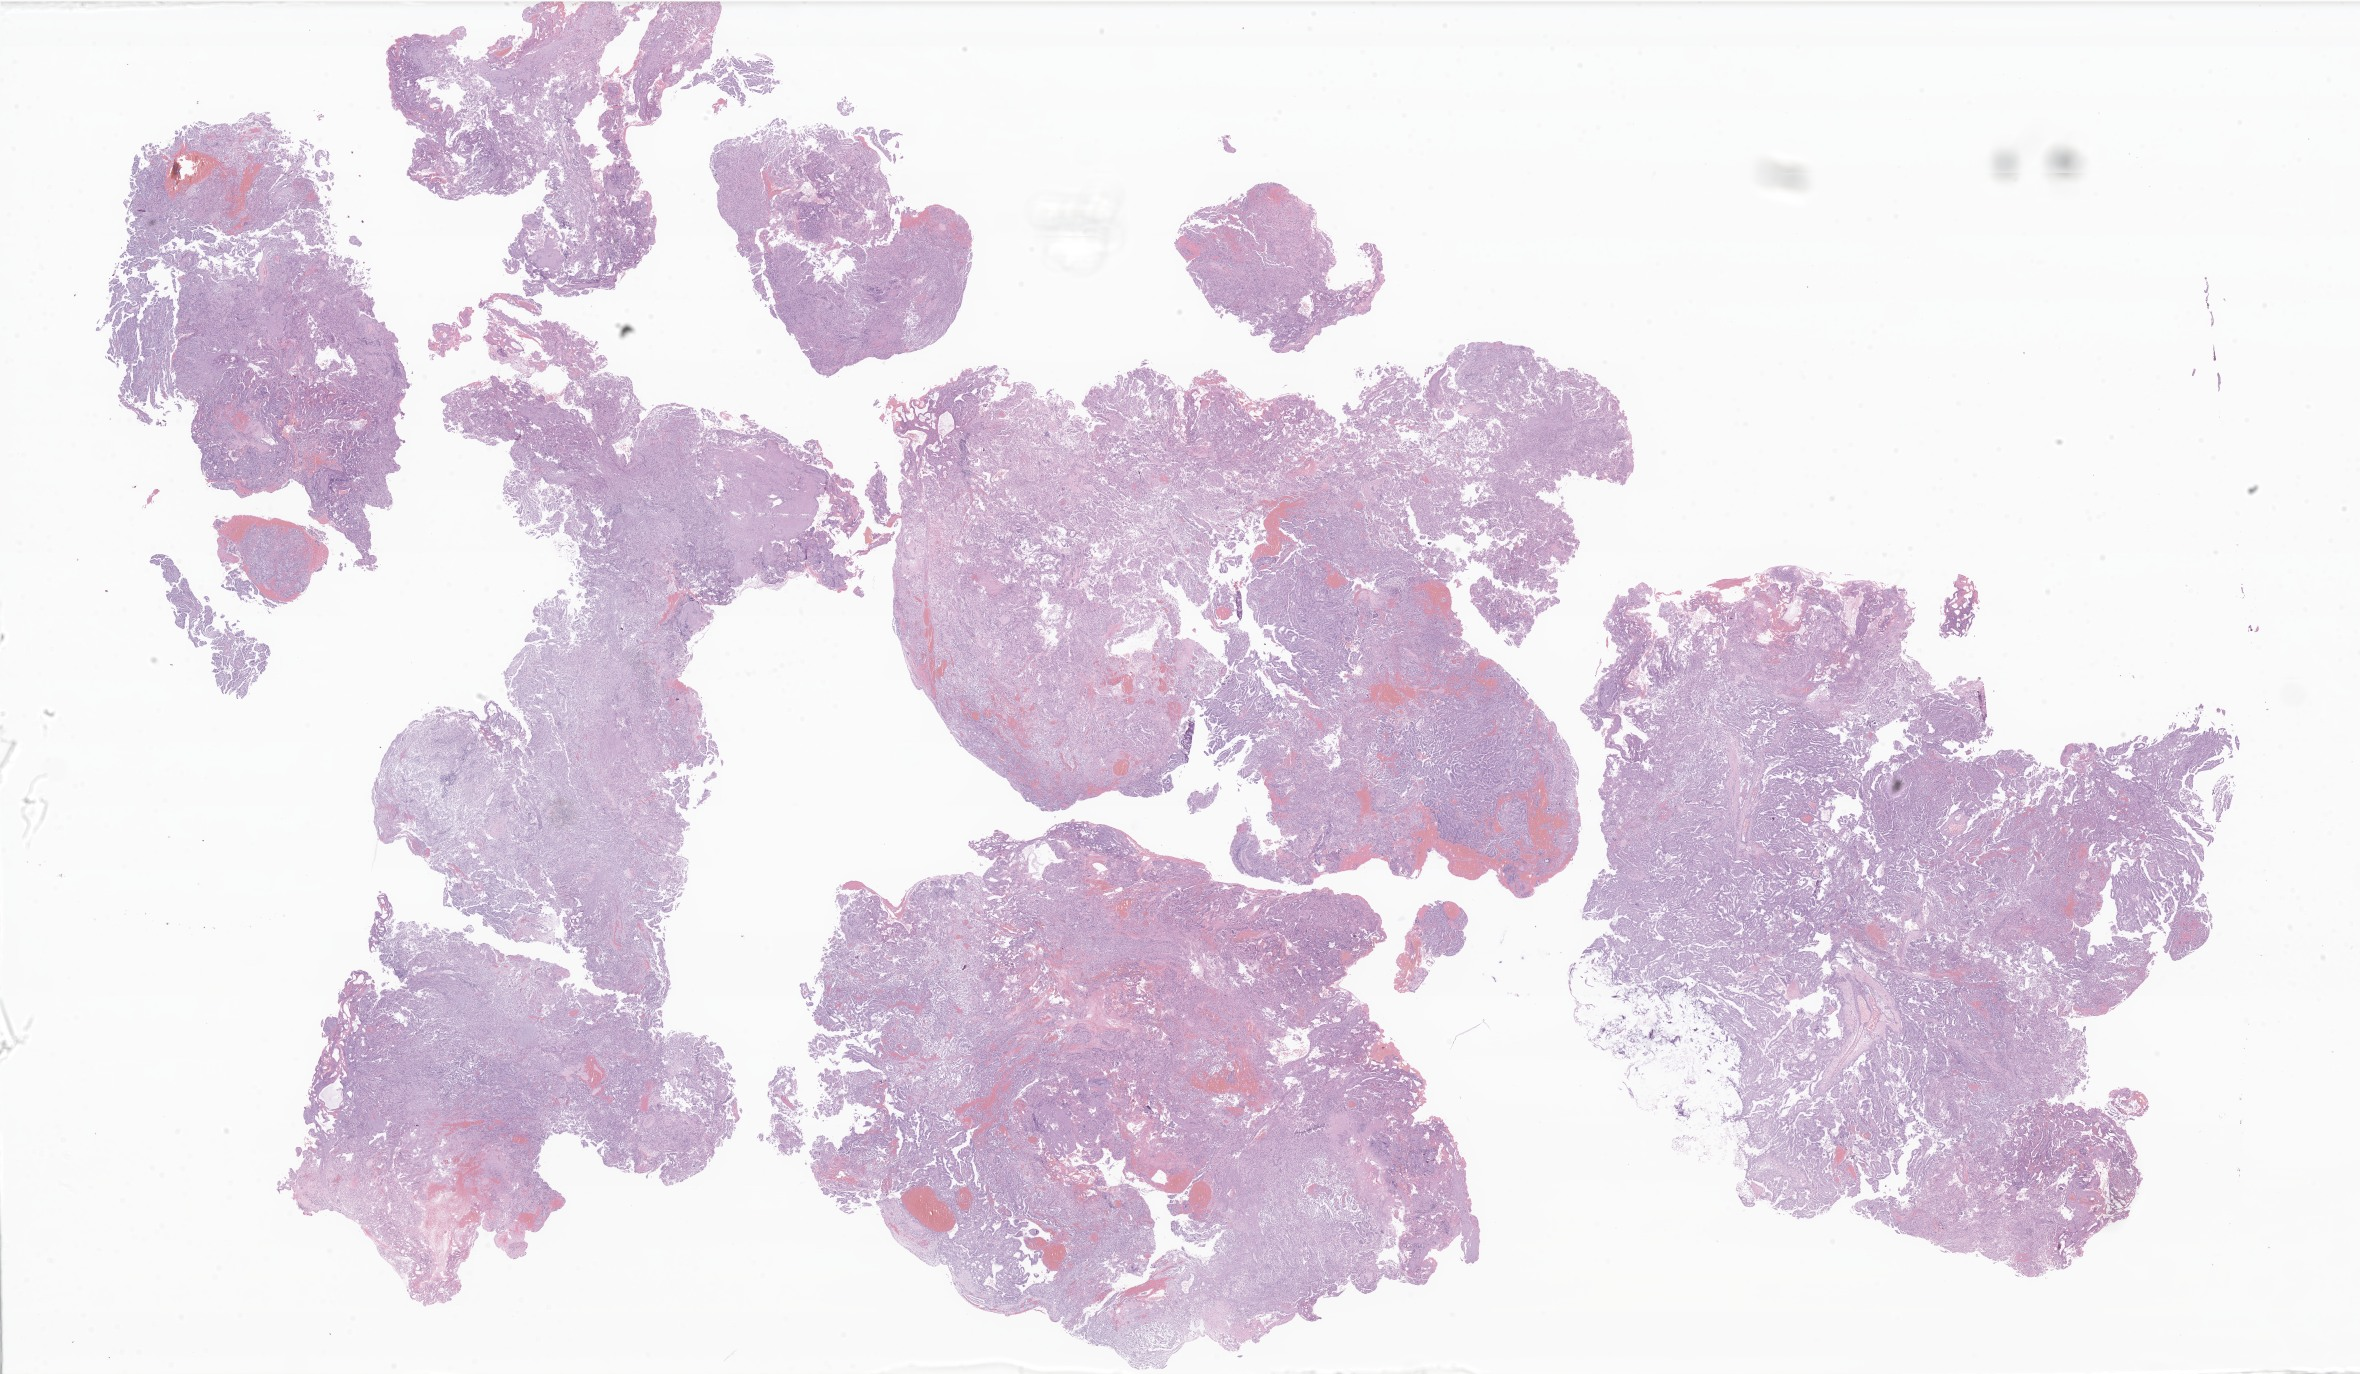
H&E whole-slide image of tumor tissue from the brain — shown as a low-resolution overview of the whole scanned area (about 39.8 x 23.2 mm). FFPE section. Patient: female, age 52 months (4 years 4 months).
- diagnosis (ICD-O-3 morphology term): Atypical choroid plexus papilloma